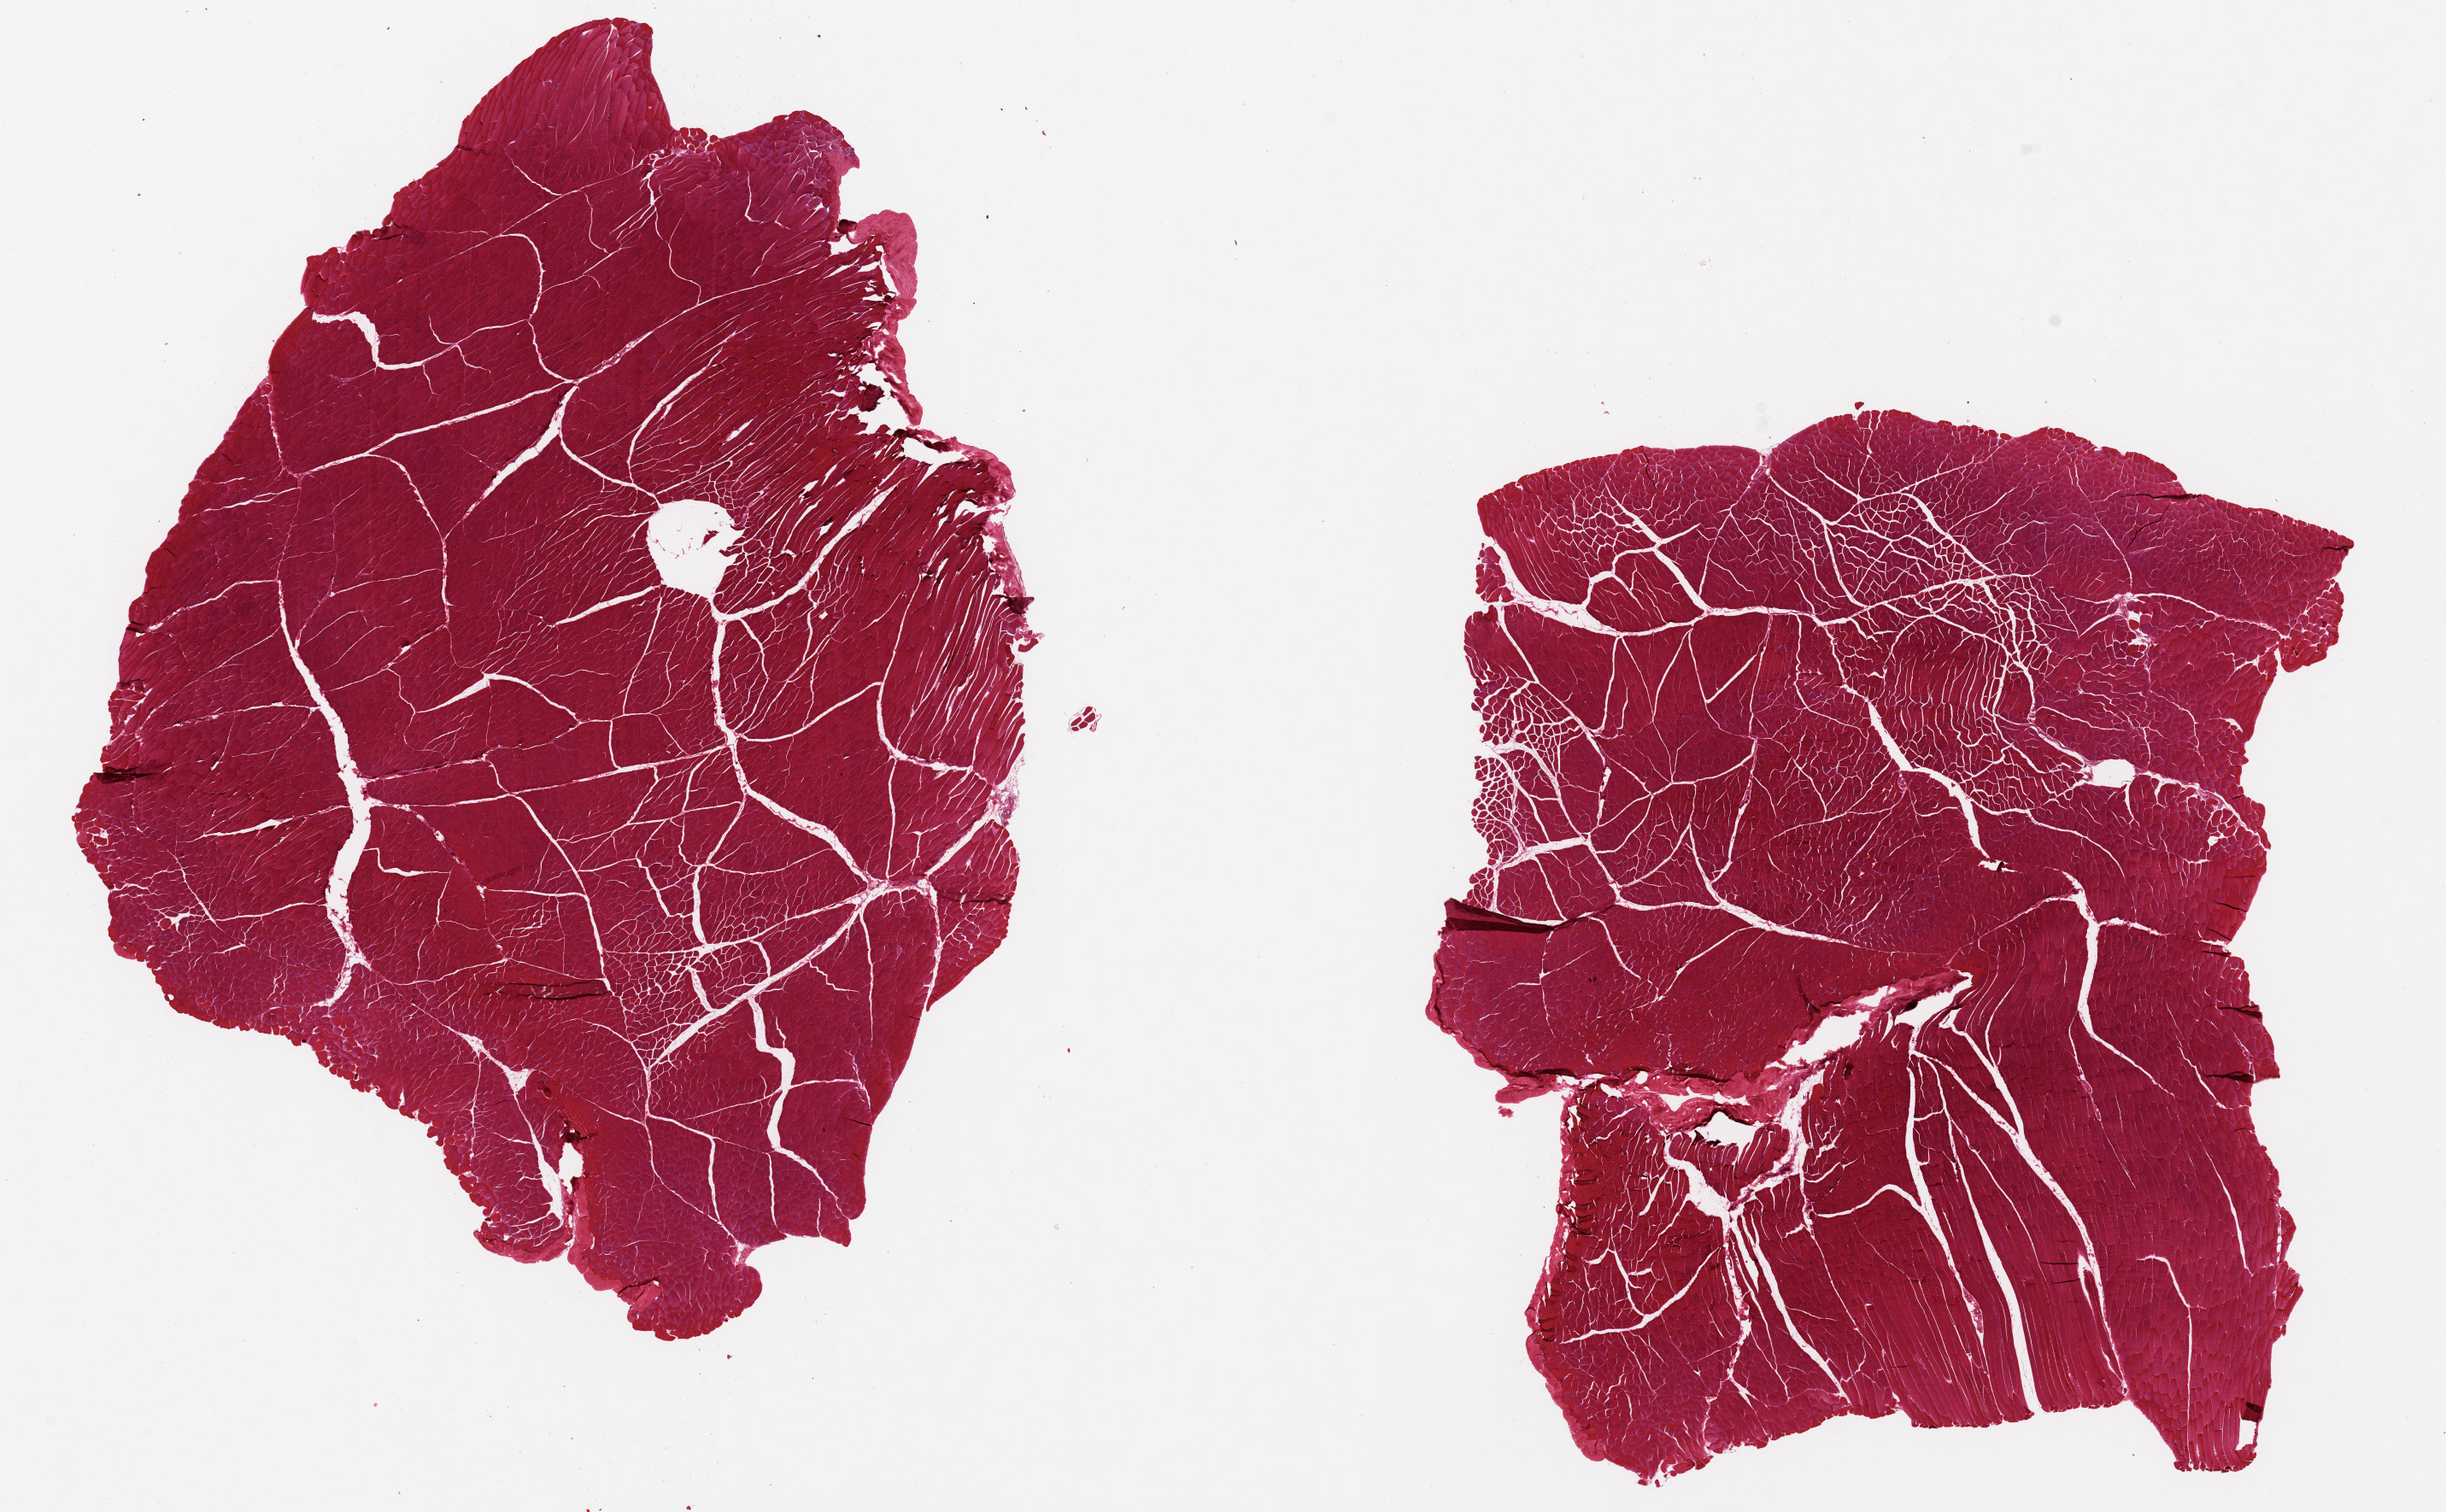
Digitized hematoxylin and eosin (H&E)-stained section — whole scanned area (about 22.6 x 14.0 mm, acquisition: 20x scan) shown as a low-resolution overview. PAXgene-fixed, paraffin-embedded tissue. Target tissue: skeletal muscle. Donor tissue sample. Donor: male.
Review note (as recorded): 2 pieces, 10x8.6 & 9.4x7.9 mm.